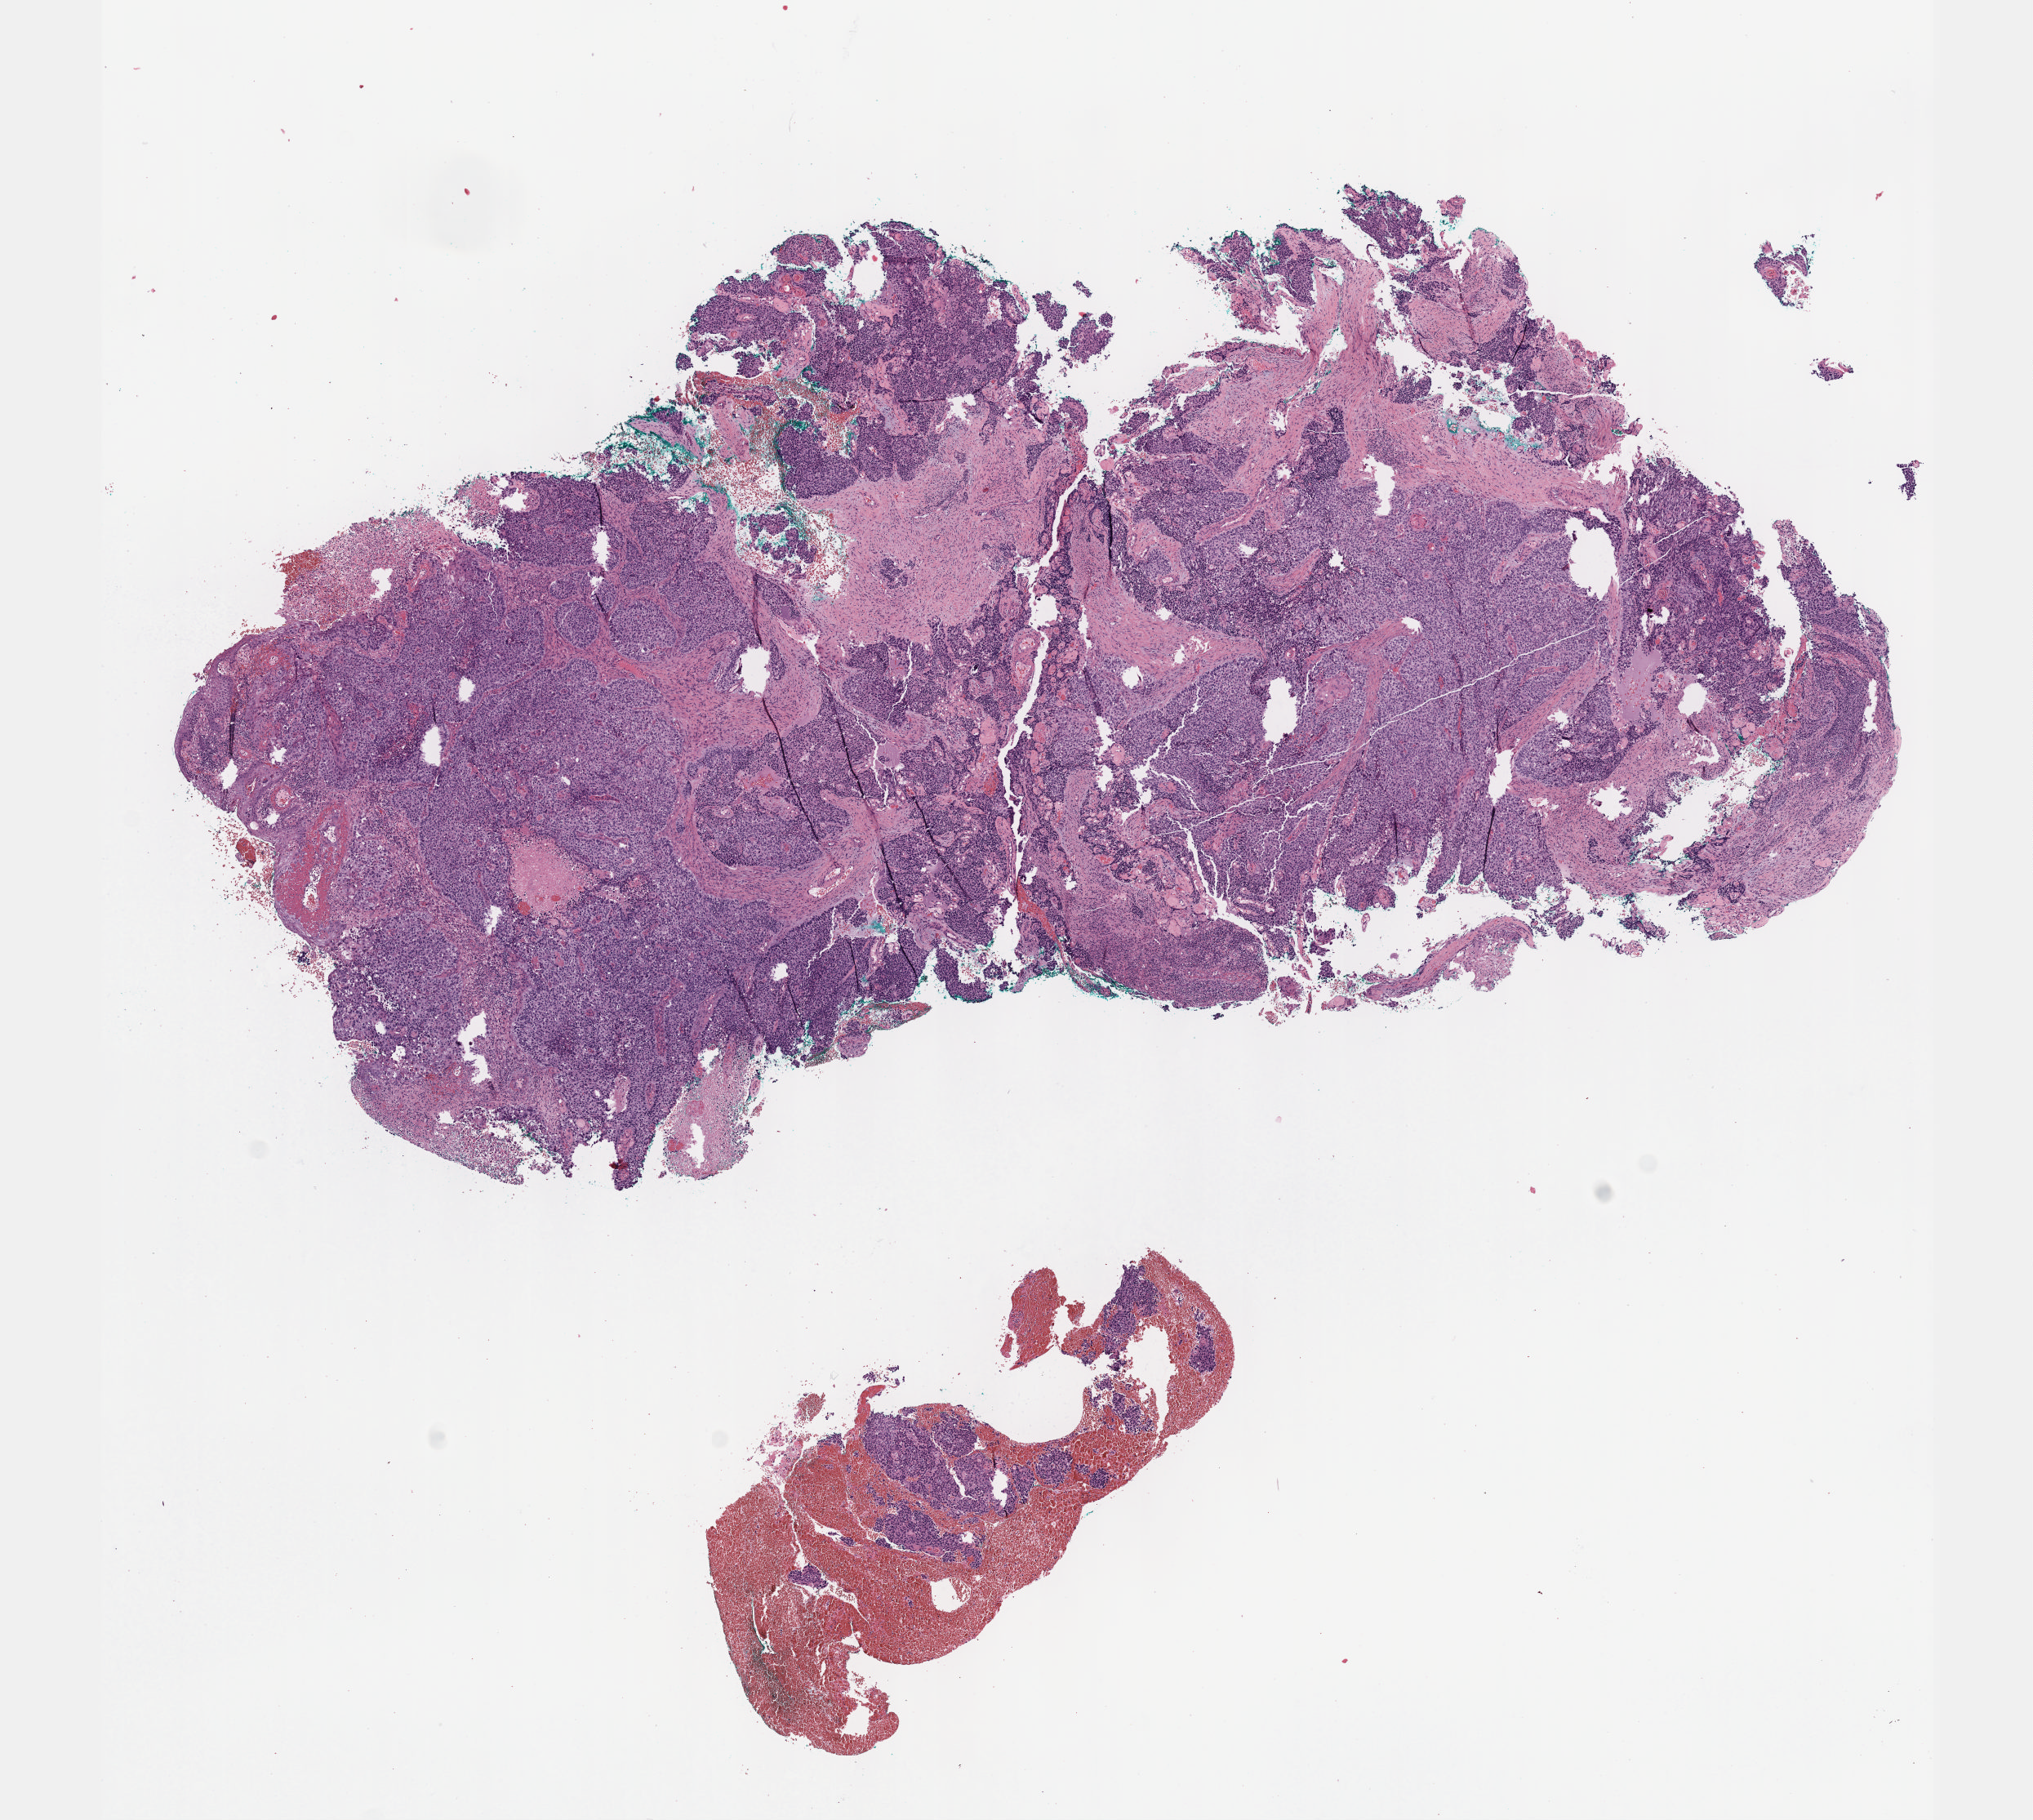
Digitized H&E tissue section (whole slide), whole scanned area (about 10.1 x 9.0 mm, acquisition: 40x scan) shown as a low-resolution overview; formalin-fixed paraffin-embedded (FFPE) diagnostic section; primary tumour sample from the cervix. Female, age 55 years at initial diagnosis. Histologic grade: G2 (moderately differentiated).
FIGO stage: IIIB. Histologic diagnosis: Squamous cell carcinoma, NOS (cervix uteri).